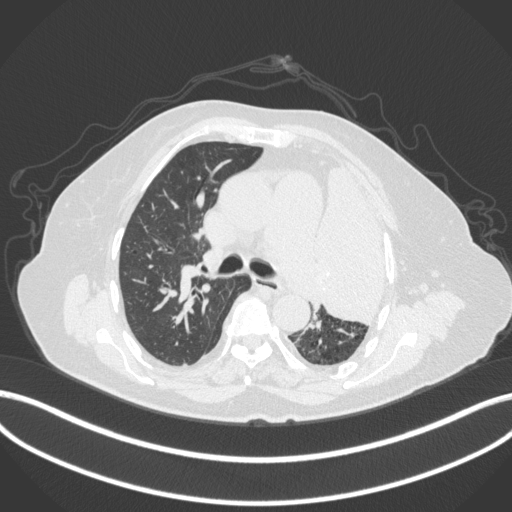
Chest CT, one axial slice; position 248 of 399 along the scan axis; lung window (W 1500 / L -600 HU); 1 mm slice thickness; 512 × 512 image matrix, field of view 400 × 400 mm. Female patient, age 75 years. From the clinical record (not read from this slice): clinical TNM (as recorded): T3 N3 M1.
Annotated regions visible in this slice (rectangle marked by the reading radiologist):
- lung tumour (recorded histology: adenocarcinoma): bounding box <308,148,395,335> (left, top, right, bottom; pixels)